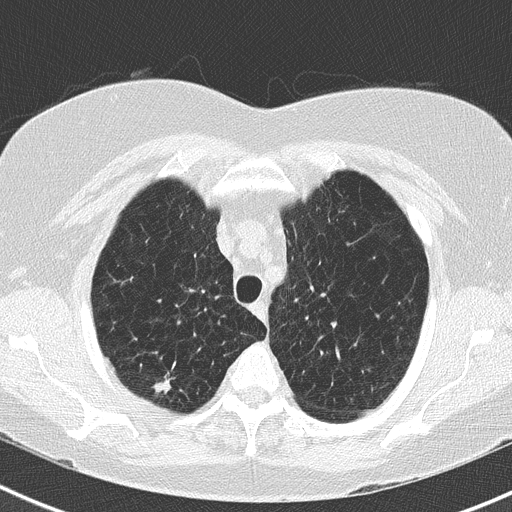
Chest CT (low-dose screening protocol), one axial image, second screening round (one year after baseline), lung window (W 1500 / L -600 HU), 2 mm slice thickness, slice 42 of 183 in the series. Female, age 73 years at enrolment. Former smoker at enrolment.
Lesion marked by an expert reader, bounding box <136,358,190,404> (left, top, right, bottom; pixels). The screening reader recorded 2 non-calcified nodules or masses ≥4 mm on this exam; which of them this box marks is not recorded. Official screen result: positive, no significant change: stable abnormalities potentially related to lung cancer, unchanged since the prior screening exam. Lung cancer was diagnosed 250 days after this screen: adenocarcinoma, NOS, right upper lobe, moderately differentiated (G2), stage IB (AJCC 6th edition), 15 mm at pathology.